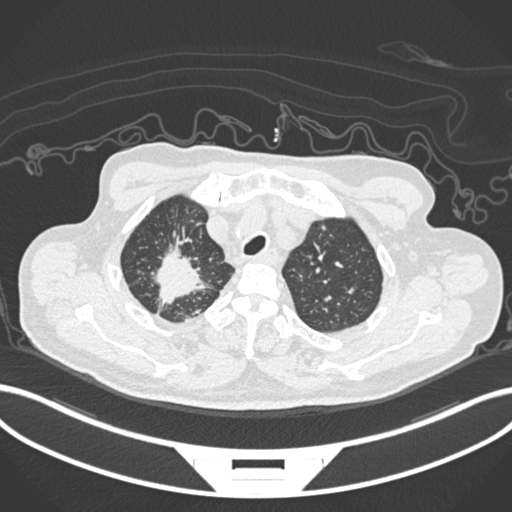
Chest CT, one axial slice. Position 183 of 207 along the scan axis. 120 kVp. Lung window (W 1500 / L -600 HU). 1 mm slice thickness. 512 × 512 image matrix, field of view 400 × 400 mm. Male patient, age 69 years. Case-level facts recorded for this patient, not image findings: clinical TNM (as recorded): T1c N1 M1.
Structures marked on this image (rectangle marked by the reading radiologist):
- lung tumour (recorded histology: adenocarcinoma): box from (x=150, y=237) to (x=212, y=311) px